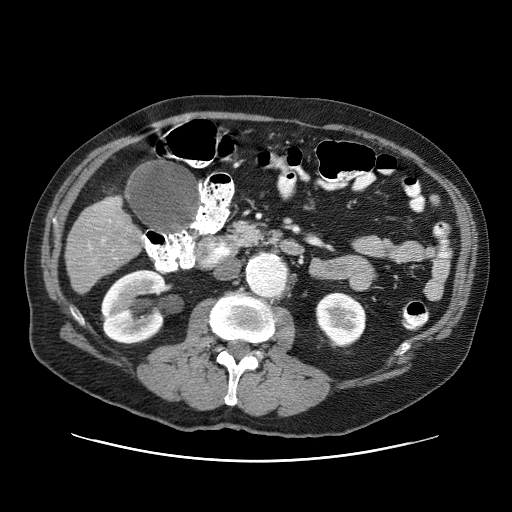
Contrast-enhanced abdominal CT (liver protocol), one axial slice. Position 14 of 87 along the scan axis. Reconstruction kernel STANDARD. One of 3 acquisitions stored at this slice position. Soft-tissue window (W 400 / L 40 HU). 2.5 mm slice thickness. 512 × 512 image matrix, field of view 400 × 400 mm. From the clinical record (not read from this slice): diagnosis: hepatocellular carcinoma (patient treated with transarterial chemoembolisation; whether this scan precedes or follows treatment is not stated here); TNM stage (as recorded): Stage-IIIA; Child-Pugh class: A; tumour nodularity: multinodular; tumour size: 6 cm.
Outlined on this slice (semi-automatic segmentation, software-assisted and operator-edited):
- liver parenchyma outside the tumour (the mass and vessels are separate outlines, so this box may not span the whole liver): bounding box (x1, y1, x2, y2) in pixels: (66, 196, 138, 294)
- liver vessels: (89, 202, 110, 248)